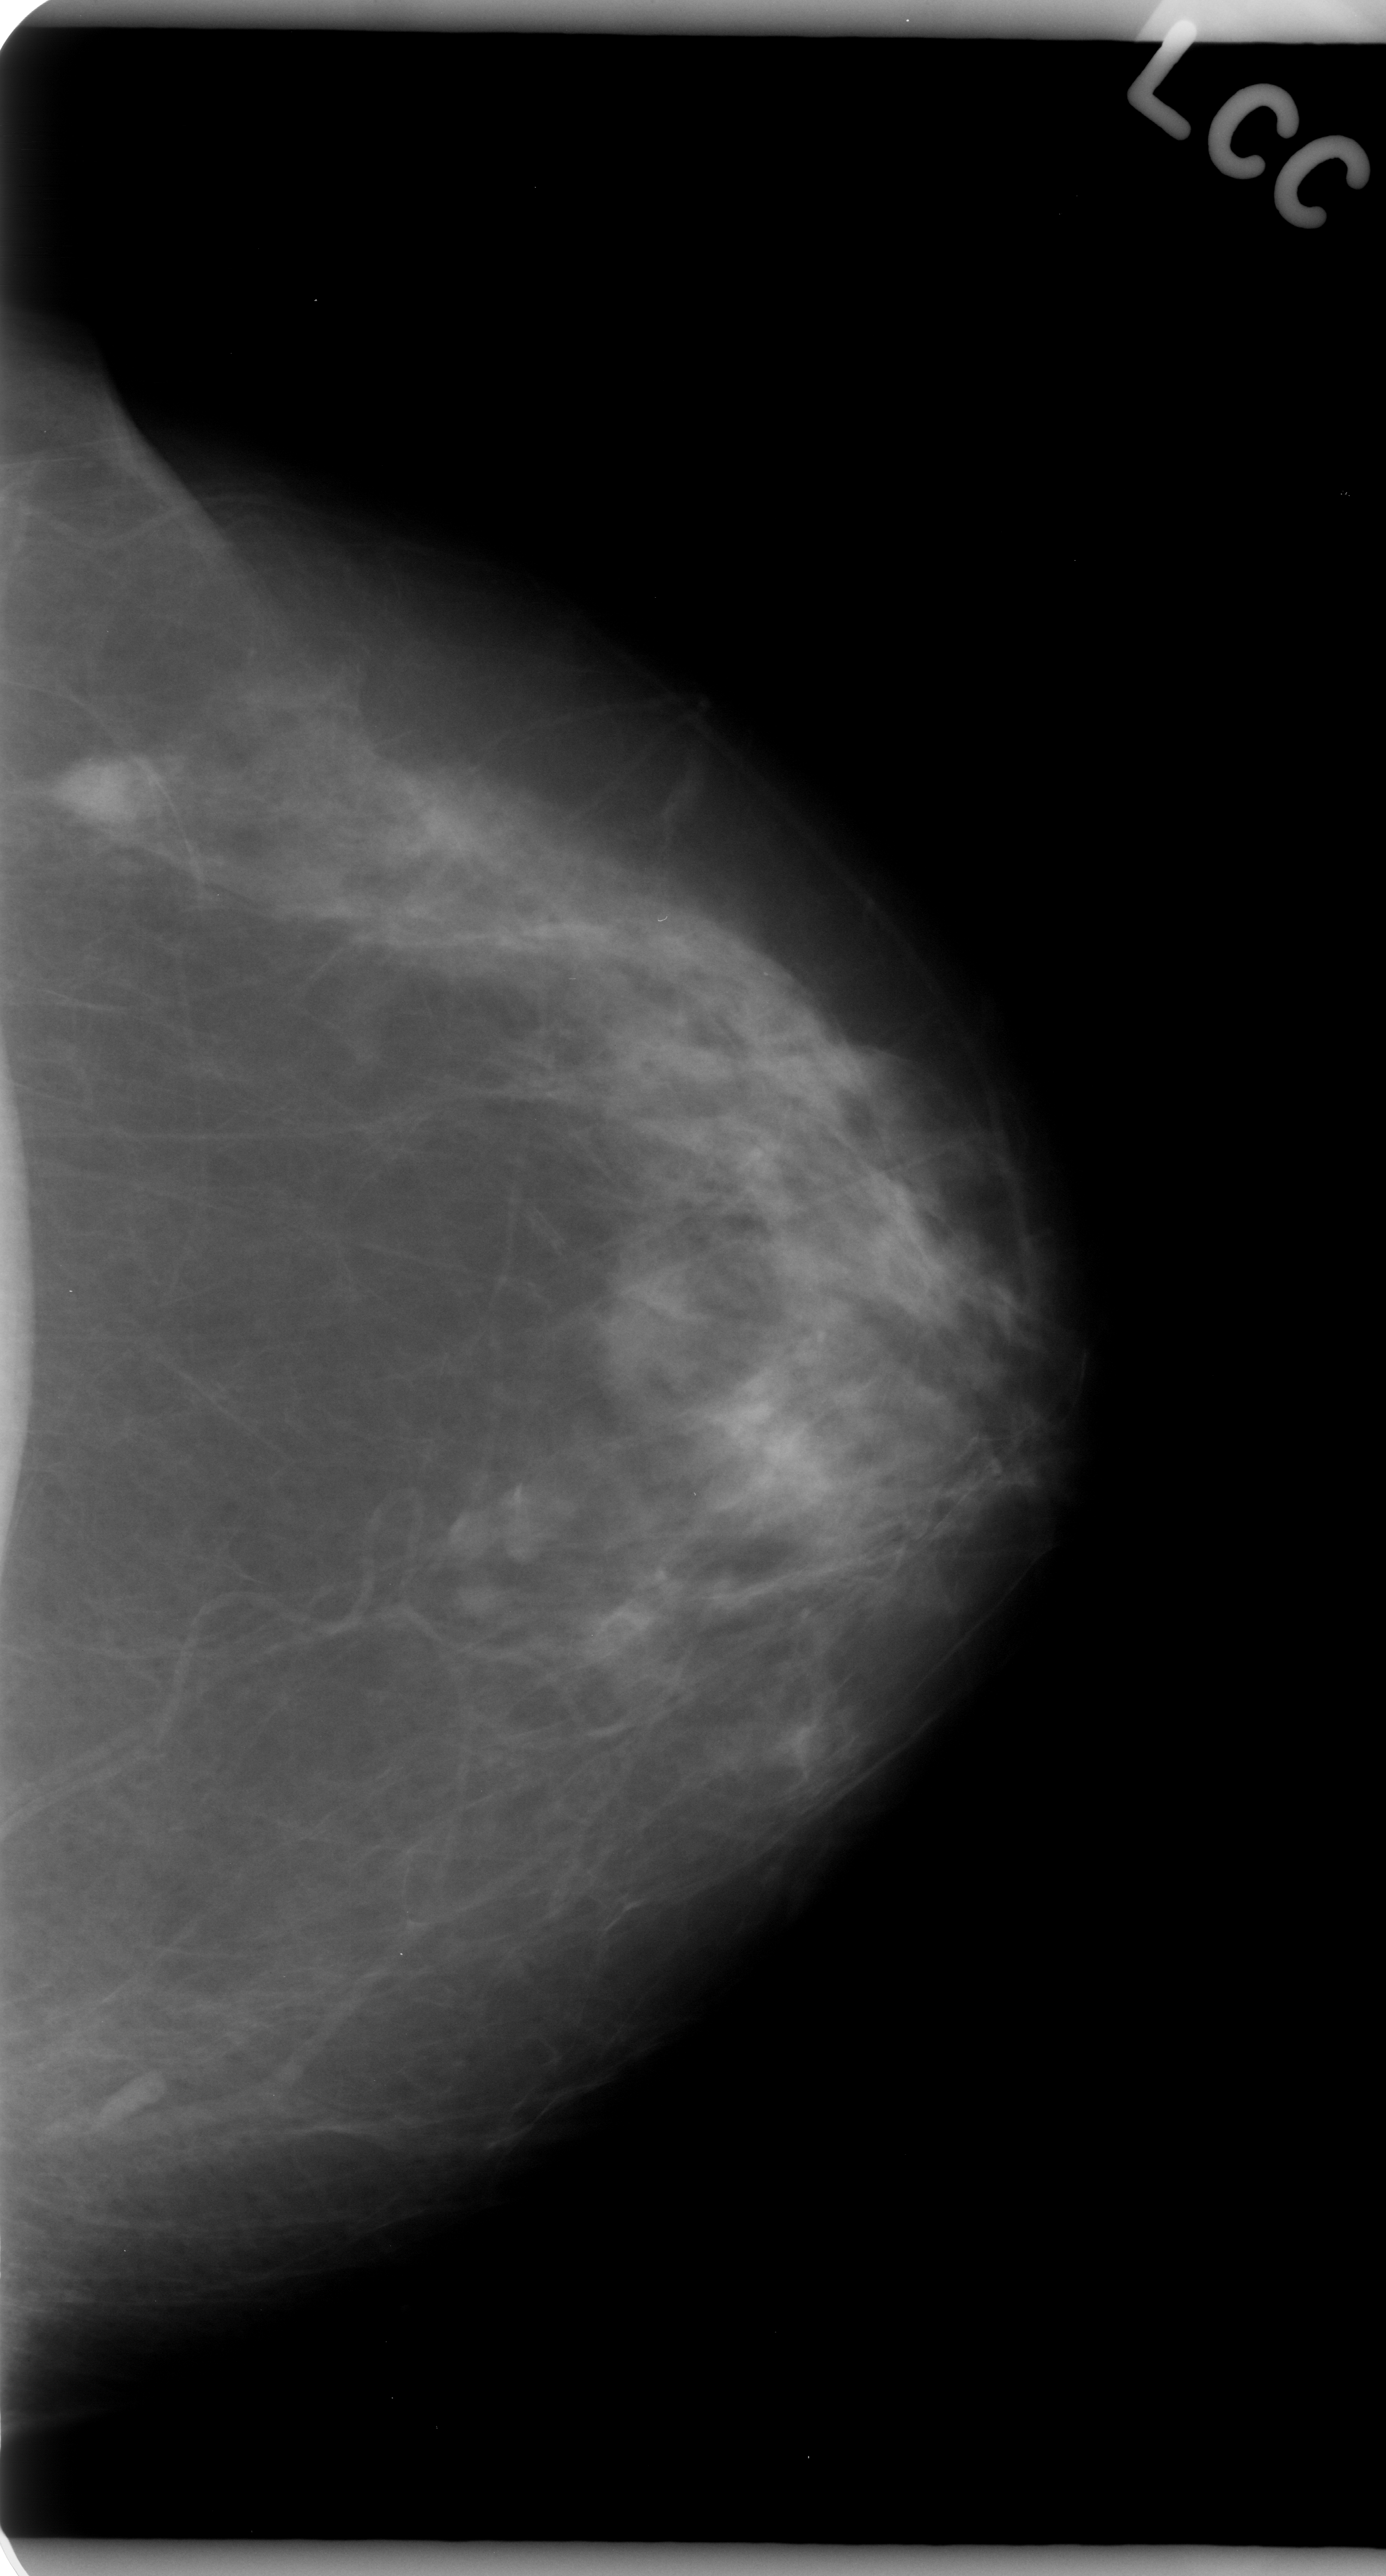
Scanned film-screen mammogram; left breast; CC view; BI-RADS breast density category 2 (scale 1–4).
Abnormality record for this image: mass, shape oval, margins microlobulated; BI-RADS assessment category 4; subtlety rating 5 on a 1 (subtle) to 5 (obvious) scale; pathology (as recorded): malignant.